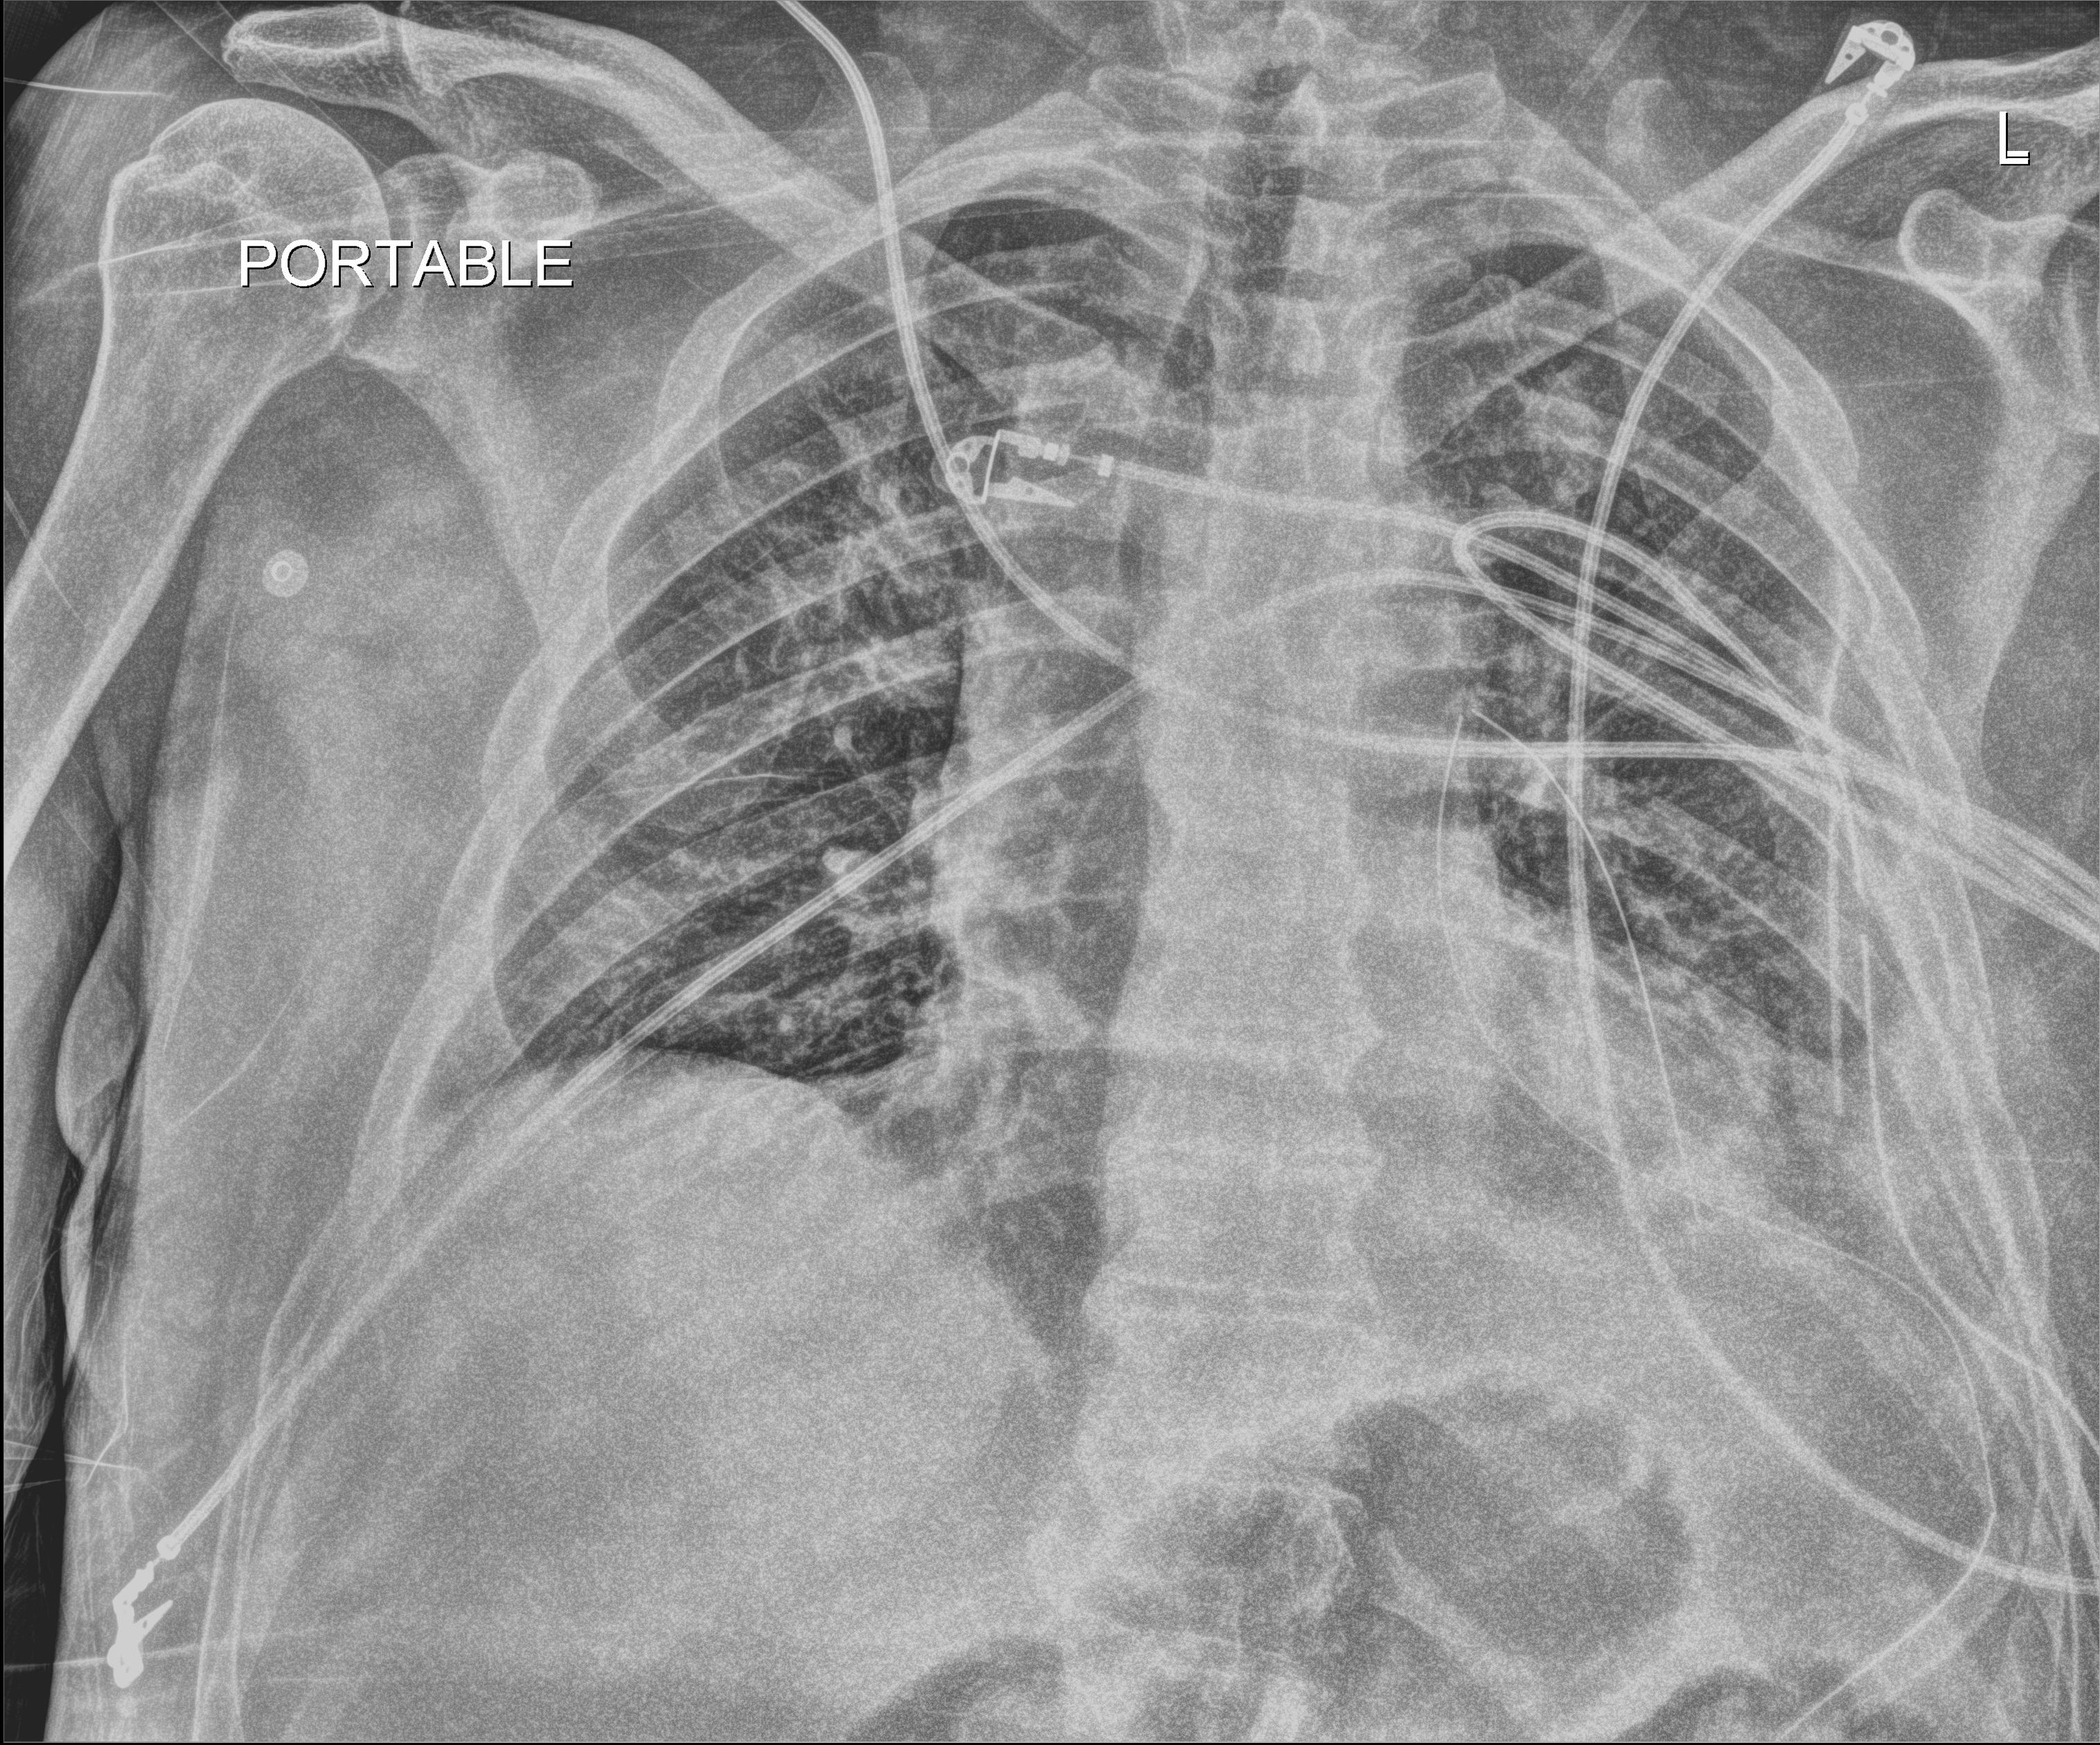
Chest X-ray (portable), anteroposterior (AP) projection. Patient hospitalised with COVID-19; male, aged 18–59 years.
From the hospital-stay record, not from the radiograph (when in the stay this image was taken is not recorded):
- mechanically ventilated during this hospital stay: no